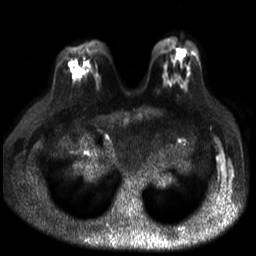
Breast MRI, one axial slice; position 13 of 30 along the scan axis; diffusion-weighted series; image 2 of 4 stored at this slice position (different b-values; order by instance number); 3 T; 256 × 256 image matrix, field of view 320 × 320 mm. Female patient.
Annotated regions visible in this slice (expert manual segmentation):
- tumour on diffusion-weighted imaging: bounding box [x1, y1, x2, y2] px = [73, 68, 82, 79]